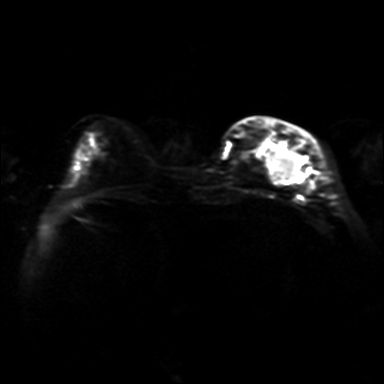
Breast MRI, one axial slice. Position 9 of 36 along the scan axis. Diffusion-weighted series; image 2 of 4 stored at this slice position (different b-values; order by instance number). 3 T. 4 mm slice thickness. 384 × 384 image matrix, field of view 320 × 320 mm. Female patient.
Structures marked on this image (expert manual segmentation):
- tumour on diffusion-weighted imaging: bounding box <271,152,301,180> (left, top, right, bottom; pixels)